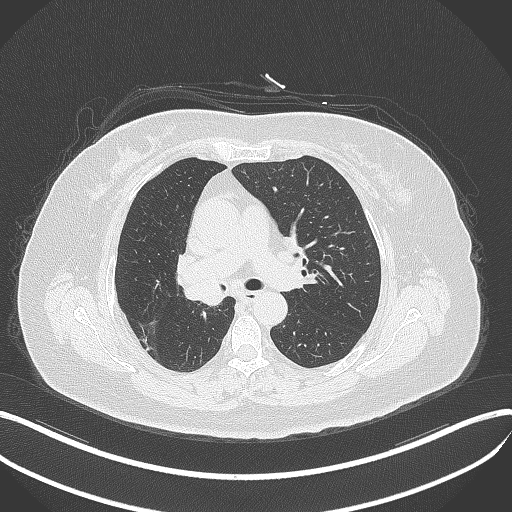
Chest CT, one axial slice. Position 221 of 376 along the scan axis. Reconstruction kernel B70f. 120 kVp. Lung window (W 1500 / L -600 HU). 512 × 512 image matrix, field of view 400 × 400 mm. Patient: female, 60 years. From the clinical record (not read from this slice): clinical TNM (as recorded): T1c N0 M0.
Outlined on this slice (rectangle marked by the reading radiologist):
- lung tumour (recorded histology: squamous cell carcinoma): bounding box (x1, y1, x2, y2) in pixels: (183, 264, 227, 309)